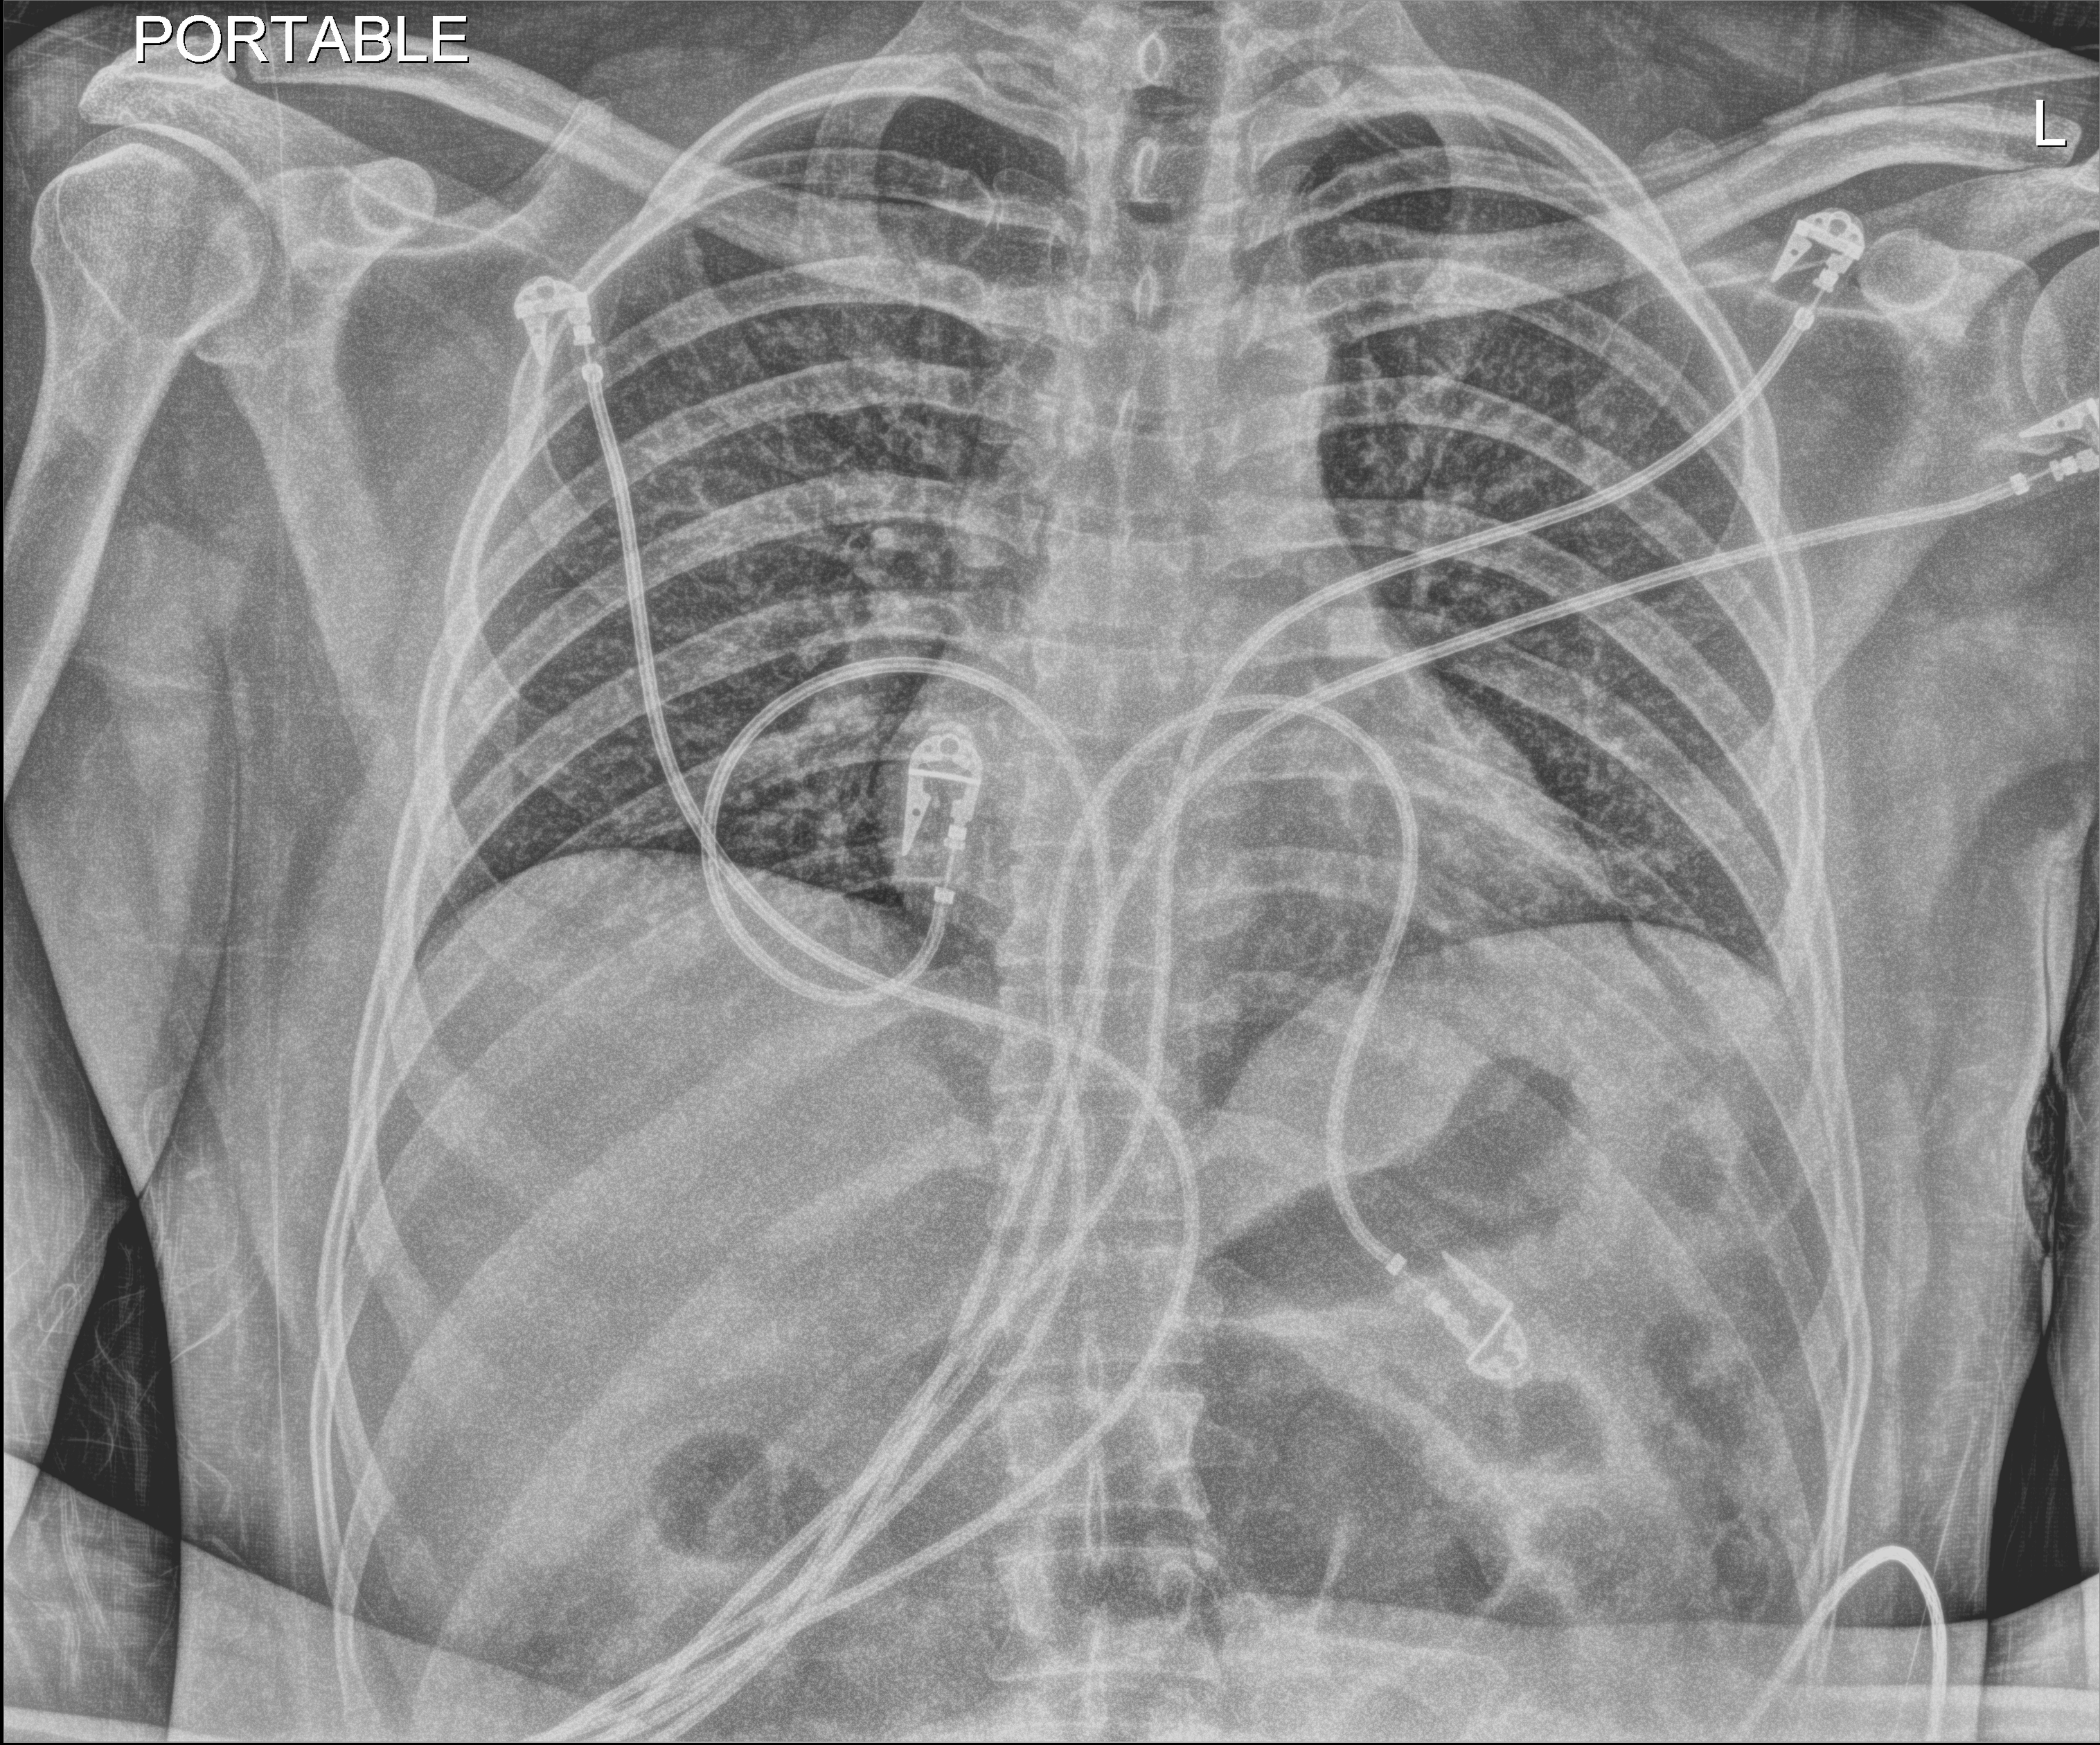
Chest X-ray (portable), anteroposterior (AP) projection. Patient hospitalised with COVID-19; male, aged 18–59 years.
Admission-level facts for this patient (not findings on this image; timing relative to this image not recorded): mechanically ventilated during this hospital stay: no.